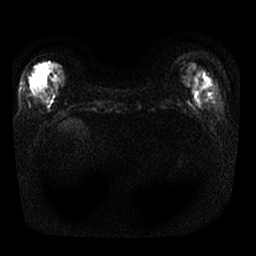
Breast MRI, one axial slice. Position 6 of 25 along the scan axis. Diffusion-weighted series; image 2 of 4 stored at this slice position (different b-values; order by instance number). 1.5 T. 256 × 256 image matrix, field of view 340 × 340 mm. Female patient.
Outlined on this slice (expert manual segmentation):
- tumour on diffusion-weighted imaging: bounding box <38,69,44,77> (left, top, right, bottom; pixels)